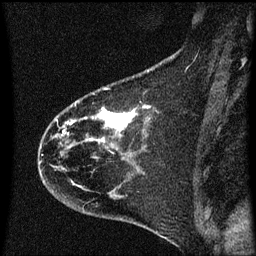
Breast MRI (dynamic contrast-enhanced), one sagittal slice; position 22 of 60 along the scan axis; dynamic contrast-enhanced series, image 2 of 3 at this slice position (ordered by acquisition); 1.5 T; TE 4.2 ms, TR 8.4 ms; 2 mm slice thickness; 256 × 256 image matrix, field of view 200 × 200 mm. Patient: female, 35 years. Case-level facts recorded for this patient, not image findings: setting: breast cancer imaged before/during neoadjuvant chemotherapy; receptor status: HER2-positive.
Structures marked on this image (semi-automatic segmentation, software-assisted and operator-edited):
- analysis volume of interest (the breast-tissue region the enhancement analysis was run in; not a lesion): box from (x=38, y=68) to (x=174, y=173) px
- tumour enhancement mask (voxels above the 70 % enhancement threshold inside the analysis volume of interest): (x=61, y=108)–(x=133, y=145)